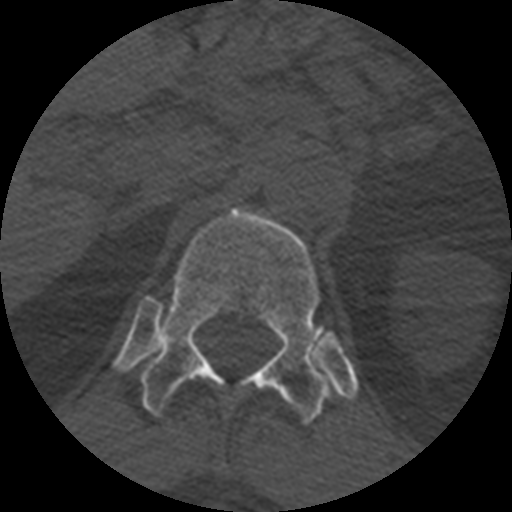
CT including the spine, one axial slice; slice 388 of 399 in the series (ordered by position); bone window (W 1800 / L 400 HU); 512 × 512 image matrix. Patient age 71 years. From the clinical record (not read from this slice): primary cancer: prostate.
Structures marked on this image (semi-automatic segmentation, software-assisted and operator-edited):
- T12 vertebra: bounding box [x1, y1, x2, y2] px = [138, 208, 334, 426]